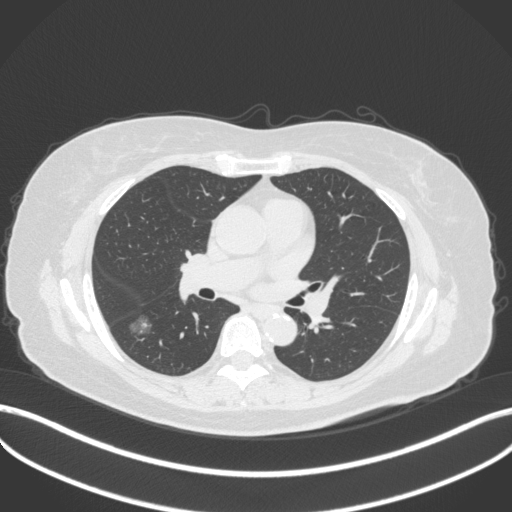
Chest CT, one axial slice; position 174 of 322 along the scan axis; reconstruction kernel B31f; 120 kVp; lung window (W 1500 / L -600 HU); 1 mm slice thickness; 512 × 512 image matrix, field of view 400 × 400 mm. Patient: female, 64 years. Case-level facts recorded for this patient, not image findings: clinical TNM (as recorded): T1c N0 M0.
Outlined on this slice (rectangle marked by the reading radiologist):
- lung tumour (recorded histology: adenocarcinoma): bounding box [x1, y1, x2, y2] px = [130, 315, 155, 337]